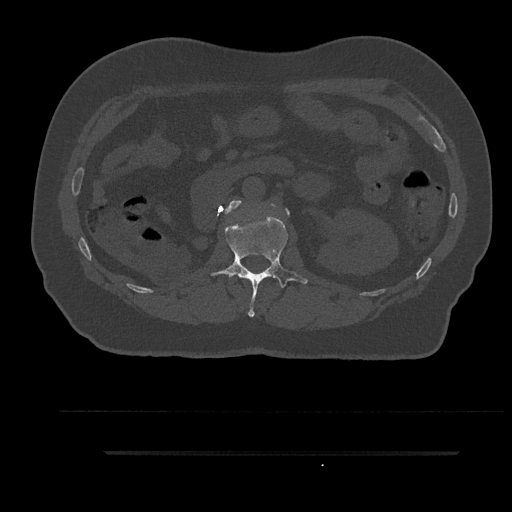
CT including the spine, one axial slice. Position 167 of 797 along the scan axis. Bone window (W 1800 / L 400 HU). 0.5 mm slice thickness. 512 × 512 image matrix, field of view 432 × 432 mm. Male patient, age 63 years. From the clinical record (not read from this slice): primary cancer: renal.
Structures marked on this image (semi-automatically segmented with operator editing):
- L1 vertebra: bounding box (x1, y1, x2, y2) in pixels: (210, 216, 308, 317)
- L2 vertebra: (225, 200, 290, 216)